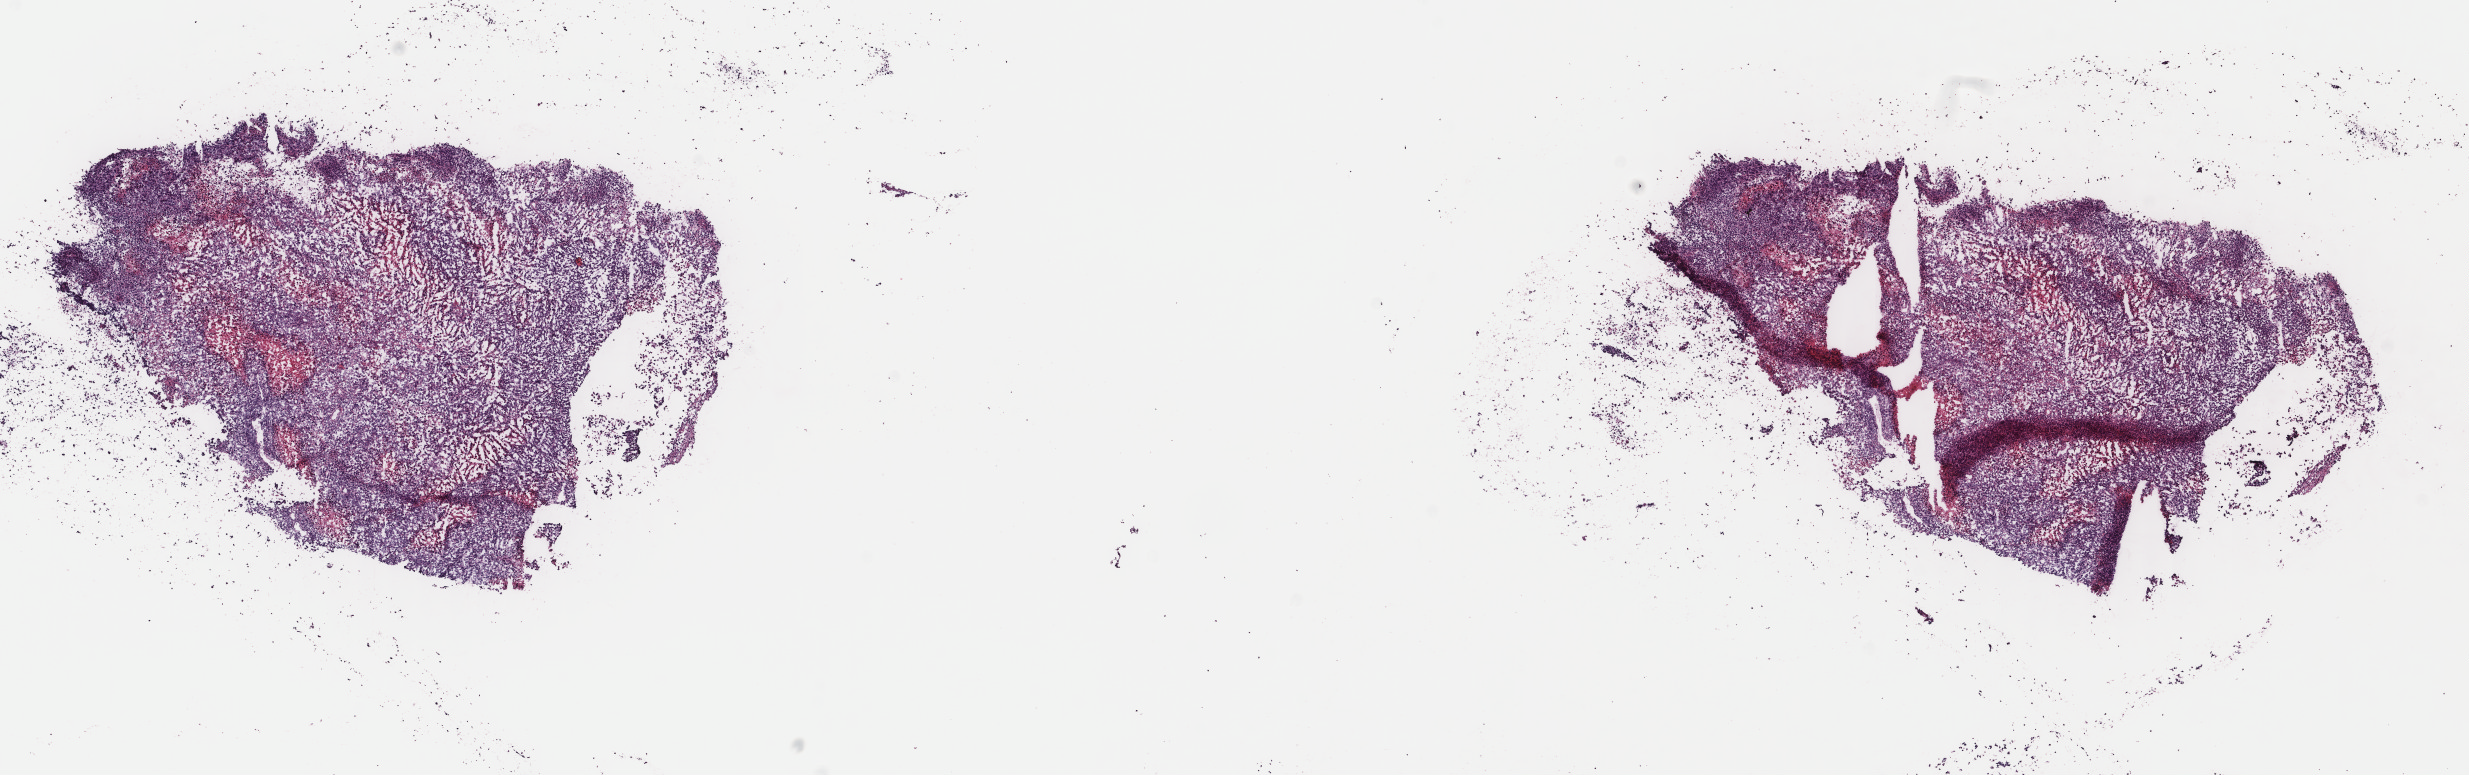
Digitized H&E tissue section (whole slide) — whole scanned area (about 19.6 x 6.2 mm, slide scanned at 40x) shown as a low-resolution overview, frozen section from the top of the tissue portion, metastatic tumour sample, sampled site: lymph nodes of axilla or arm. Male, age 61 years at initial diagnosis. Slide review estimates, as recorded: tumour cells 85%, tumour nuclei 90%, normal cells 0%, stromal cells 0%, necrosis 15%. Inflammatory infiltration, as recorded: lymphocyte infiltration 0%, monocyte infiltration 0%, neutrophil infiltration 0%.
* this section: metastatic tumour tissue
* patient diagnosis: Malignant melanoma, NOS